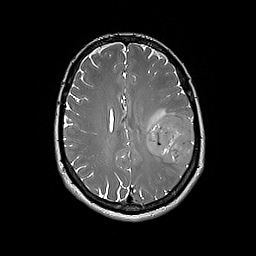
Brain MRI from a brain-tumour surgery series, one axial slice. Position 79 of 192 along the scan axis. 1 mm slice thickness. 256 × 256 image matrix, field of view 250 × 250 mm. Case-level facts recorded for this patient, not image findings: histopathology: Glioblastoma; WHO grade: 4.
Annotated regions visible in this slice (manually delineated by an expert):
- tumour: bounding box [x1, y1, x2, y2] px = [147, 114, 195, 166]